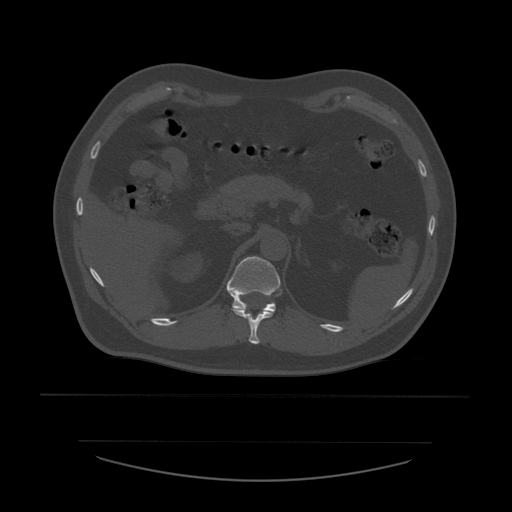
CT including the spine, one axial slice. Position 262 of 532 along the scan axis. 120 kVp. Bone window (W 1800 / L 400 HU). 512 × 512 image matrix, field of view 441 × 441 mm. Patient age 44 years. From the clinical record (not read from this slice): primary cancer: soft tissue sarcoma.
Annotated regions visible in this slice (semi-automatic segmentation, software-assisted and operator-edited):
- T11 vertebra: bounding box [x1, y1, x2, y2] px = [232, 308, 274, 345]
- T12 vertebra: [227, 256, 281, 312]